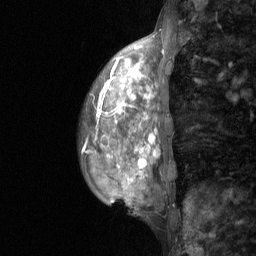
Breast MRI (dynamic contrast-enhanced), one sagittal slice; position 18 of 64 along the scan axis; dynamic contrast-enhanced study with each time point stored as its own series, time point 2 of 3 at this slice position (early post-contrast, ordered by acquisition time); 1.5 T; TE 4.8 ms, TR 27 ms; 2 mm slice thickness; 256 × 256 image matrix, field of view 200 × 200 mm. Female patient, age 36 years. From the clinical record (not read from this slice): setting: breast cancer imaged before/during neoadjuvant chemotherapy; receptor status: HR-positive, HER2-negative.
Outlined on this slice (semi-automatically segmented with operator editing):
- analysis volume of interest (the breast-tissue region the enhancement analysis was run in; not a lesion): bounding box <81,100,176,210> (left, top, right, bottom; pixels)
- tumour enhancement mask (voxels above the 90 % enhancement threshold inside the analysis volume of interest): <97,102,150,168>